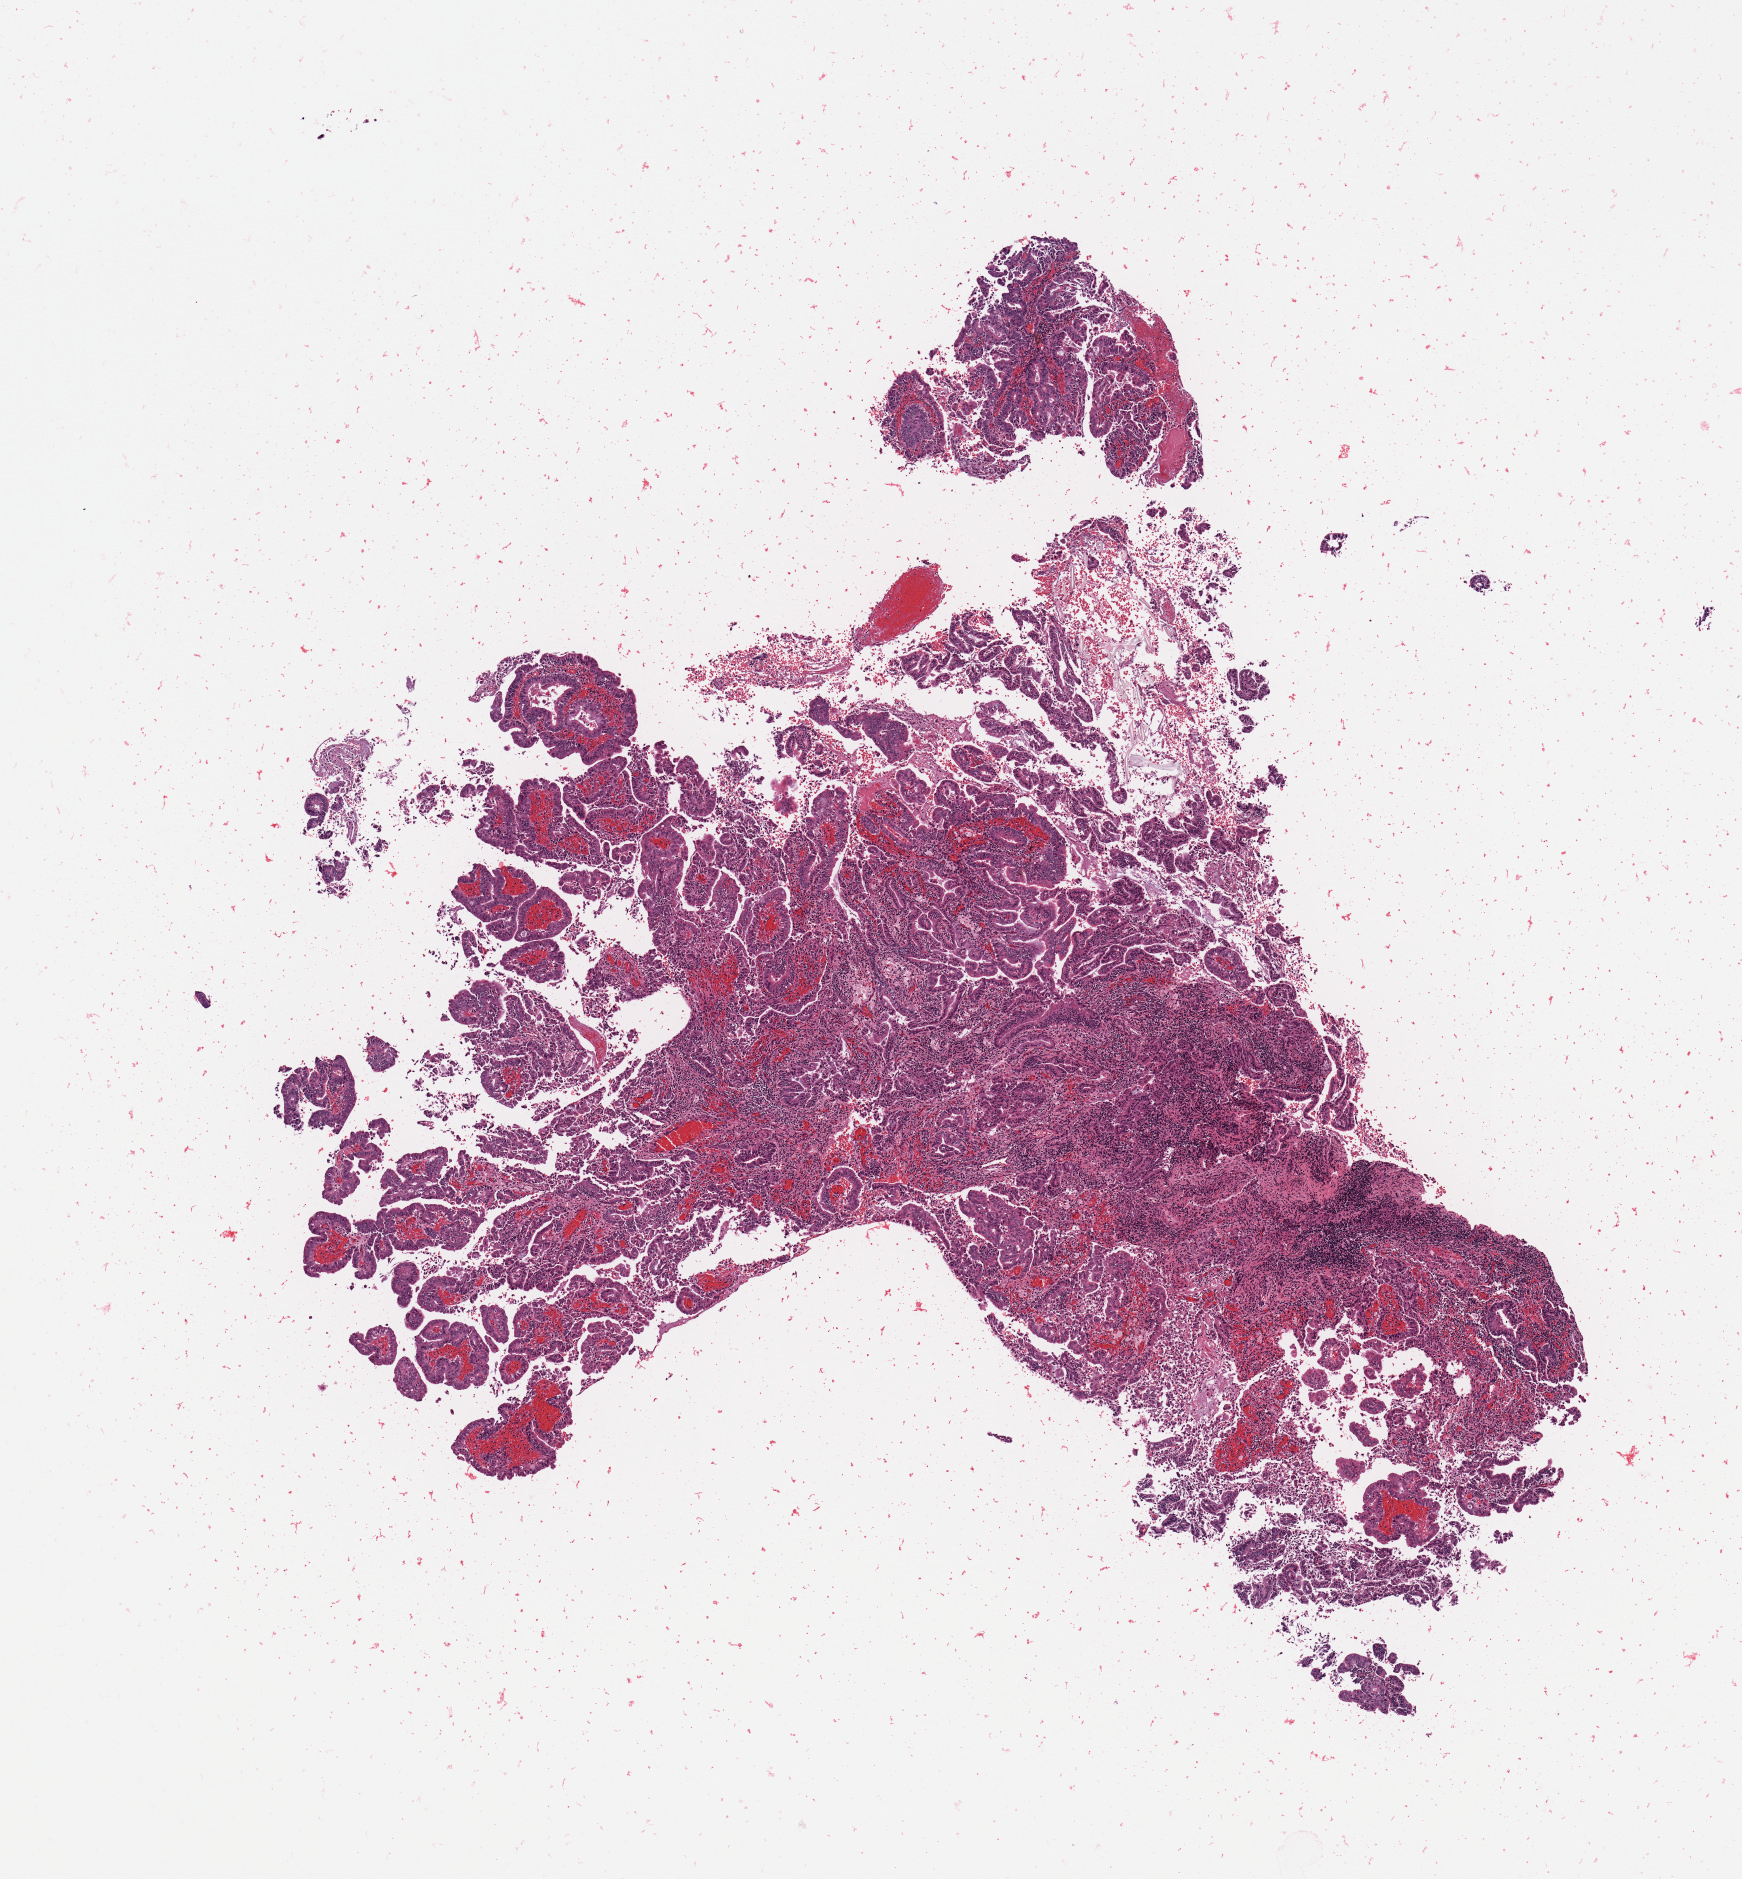
Hematoxylin and eosin (H&E) stained whole-slide image, low-resolution overview of the scanned area, about 6.9 x 7.4 mm (acquisition: 20x scan); uterus, tumour tissue. Patient: female, age 42 years. Histologic grade: G1 (well differentiated).
Histologic diagnosis: Endometrioid adenocarcinoma, NOS.